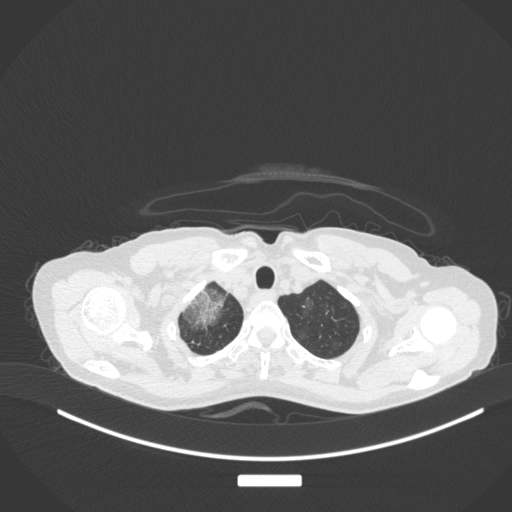
Chest CT, one axial slice; 120 kVp; lung window (W 1500 / L -600 HU); 1 mm slice thickness; 512 × 512 image matrix. Patient: female, 59 years. From the clinical record (not read from this slice): clinical TNM (as recorded): T3 N0 M0.
Structures marked on this image (rectangle marked by the reading radiologist):
- lung tumour (recorded histology: adenocarcinoma): bounding box [x1, y1, x2, y2] px = [181, 284, 229, 326]